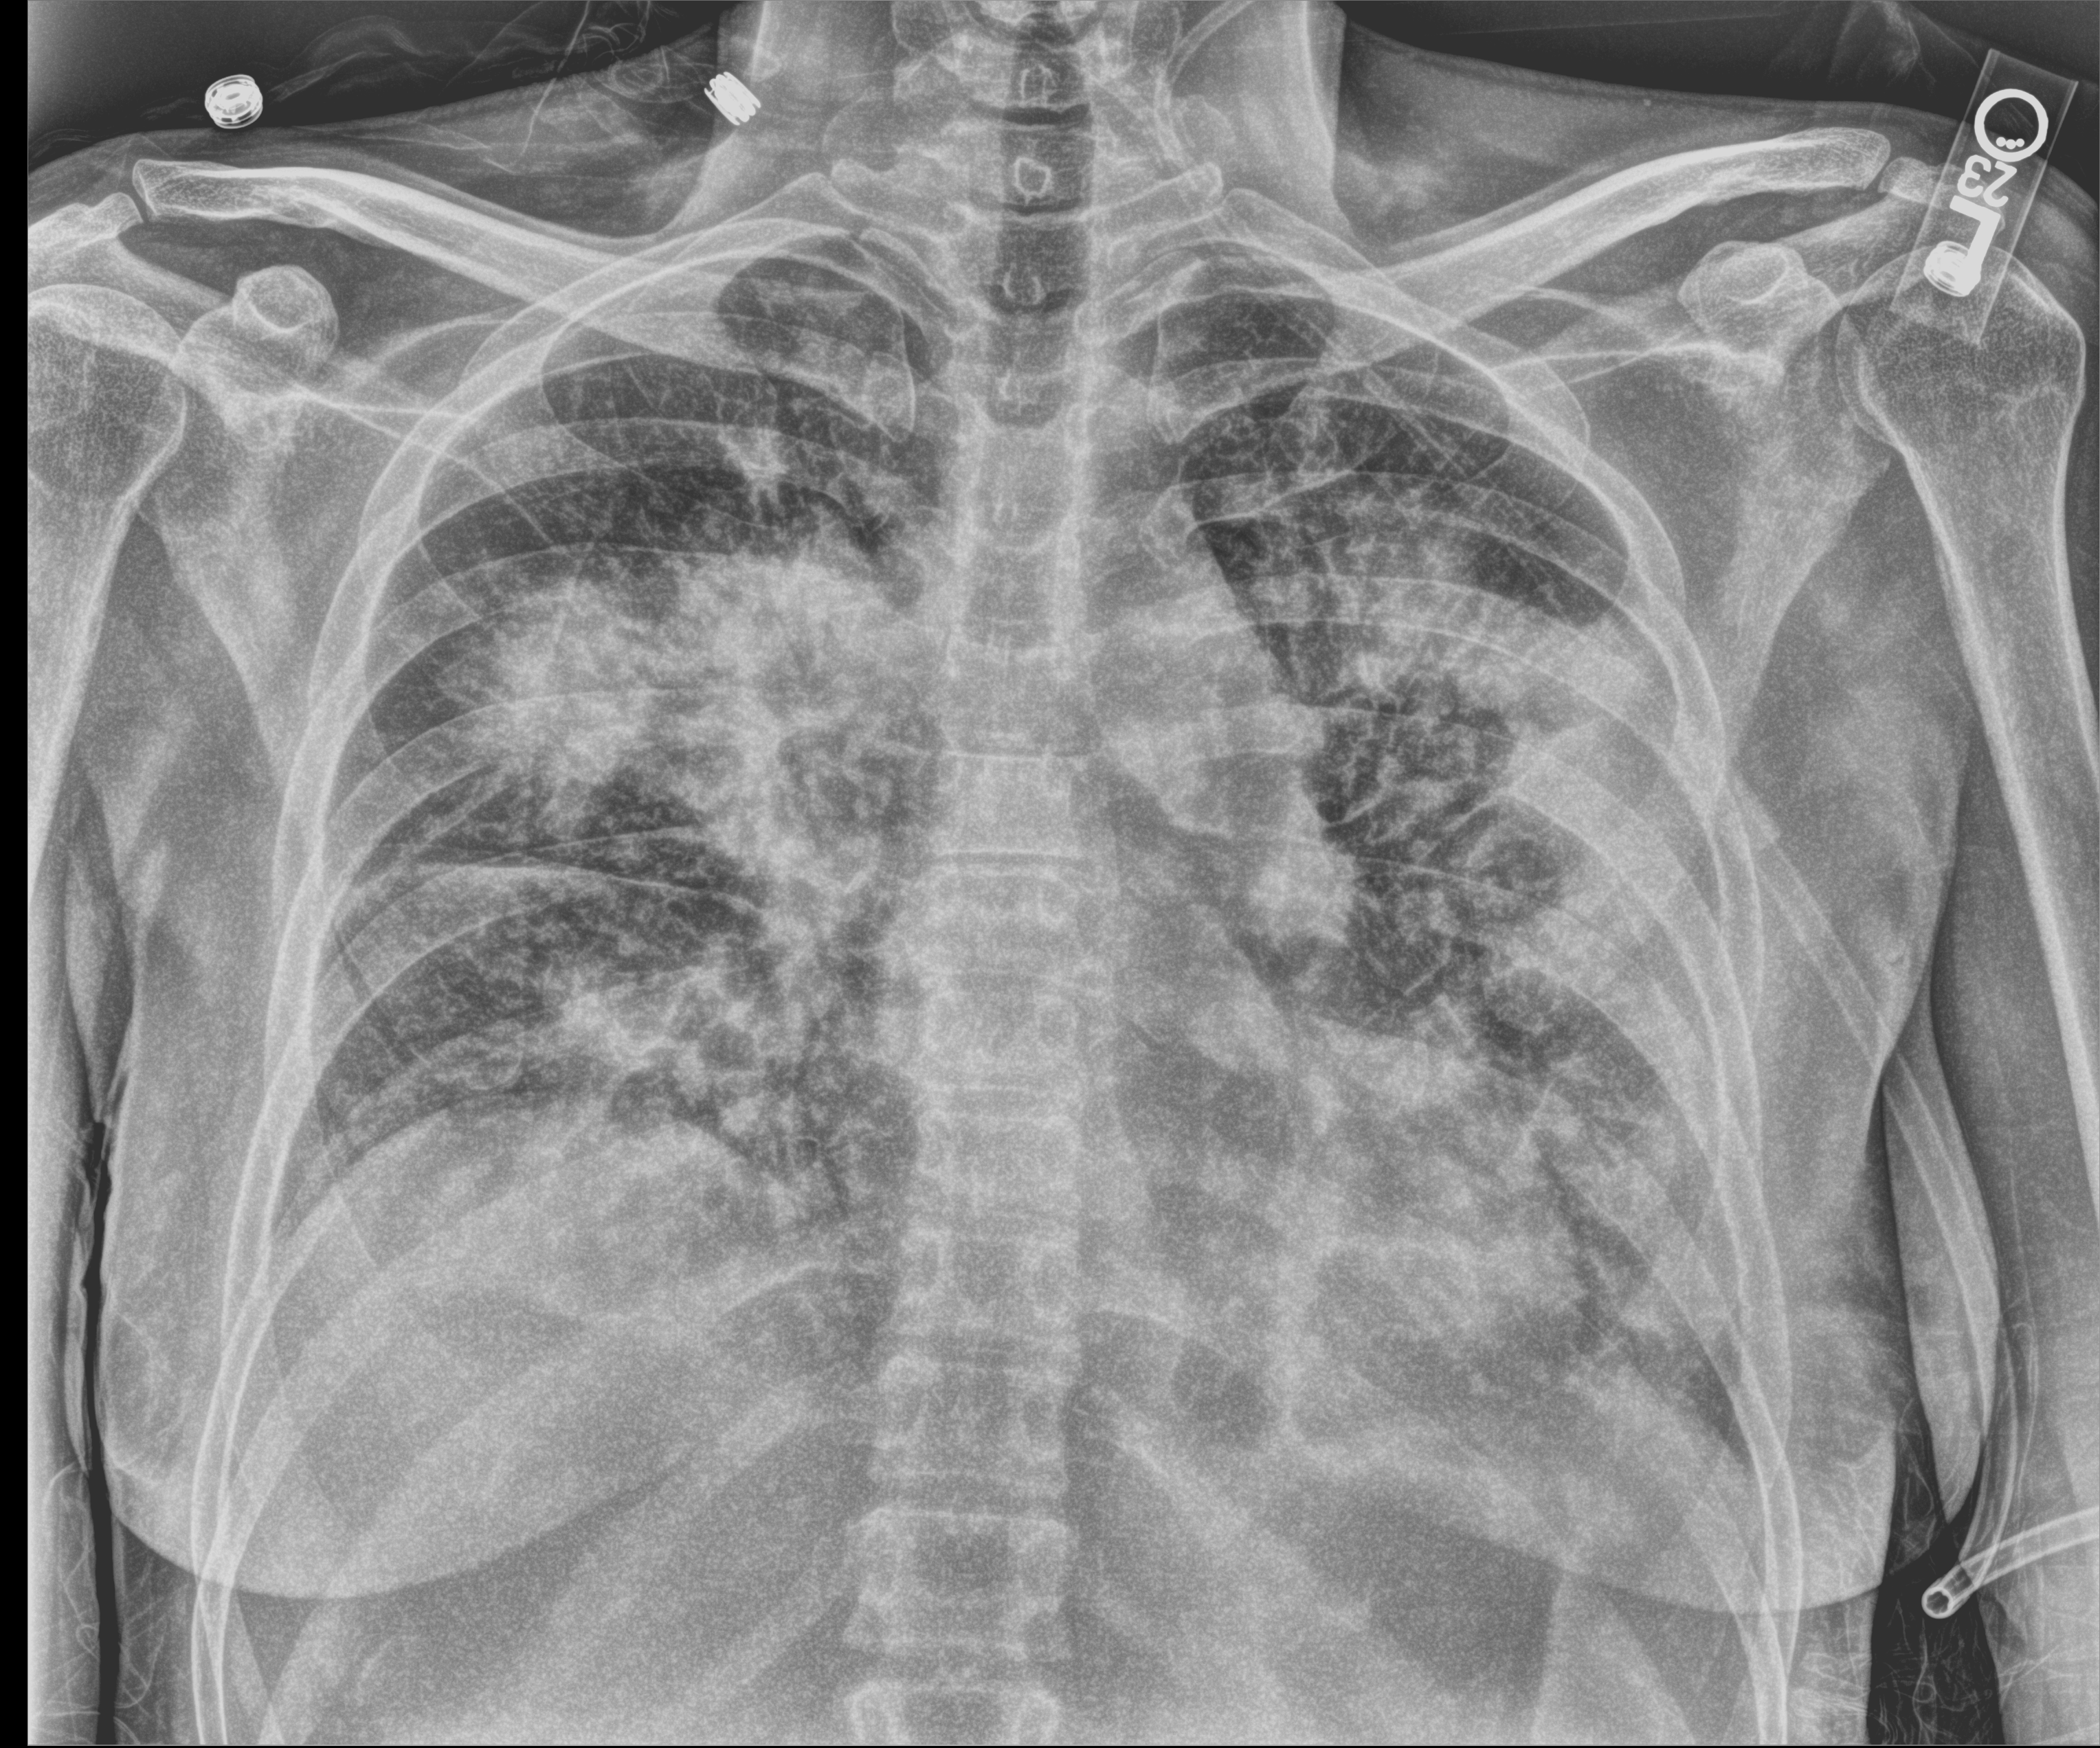
Portable chest radiograph, anteroposterior (AP) projection. Patient hospitalised with COVID-19; female, aged 18–59 years.
From the hospital-stay record, not from the radiograph (when in the stay this image was taken is not recorded):
- mechanically ventilated during this hospital stay: no
- admitted to intensive care during this hospital stay: yes
- chronic kidney disease (admission record): no